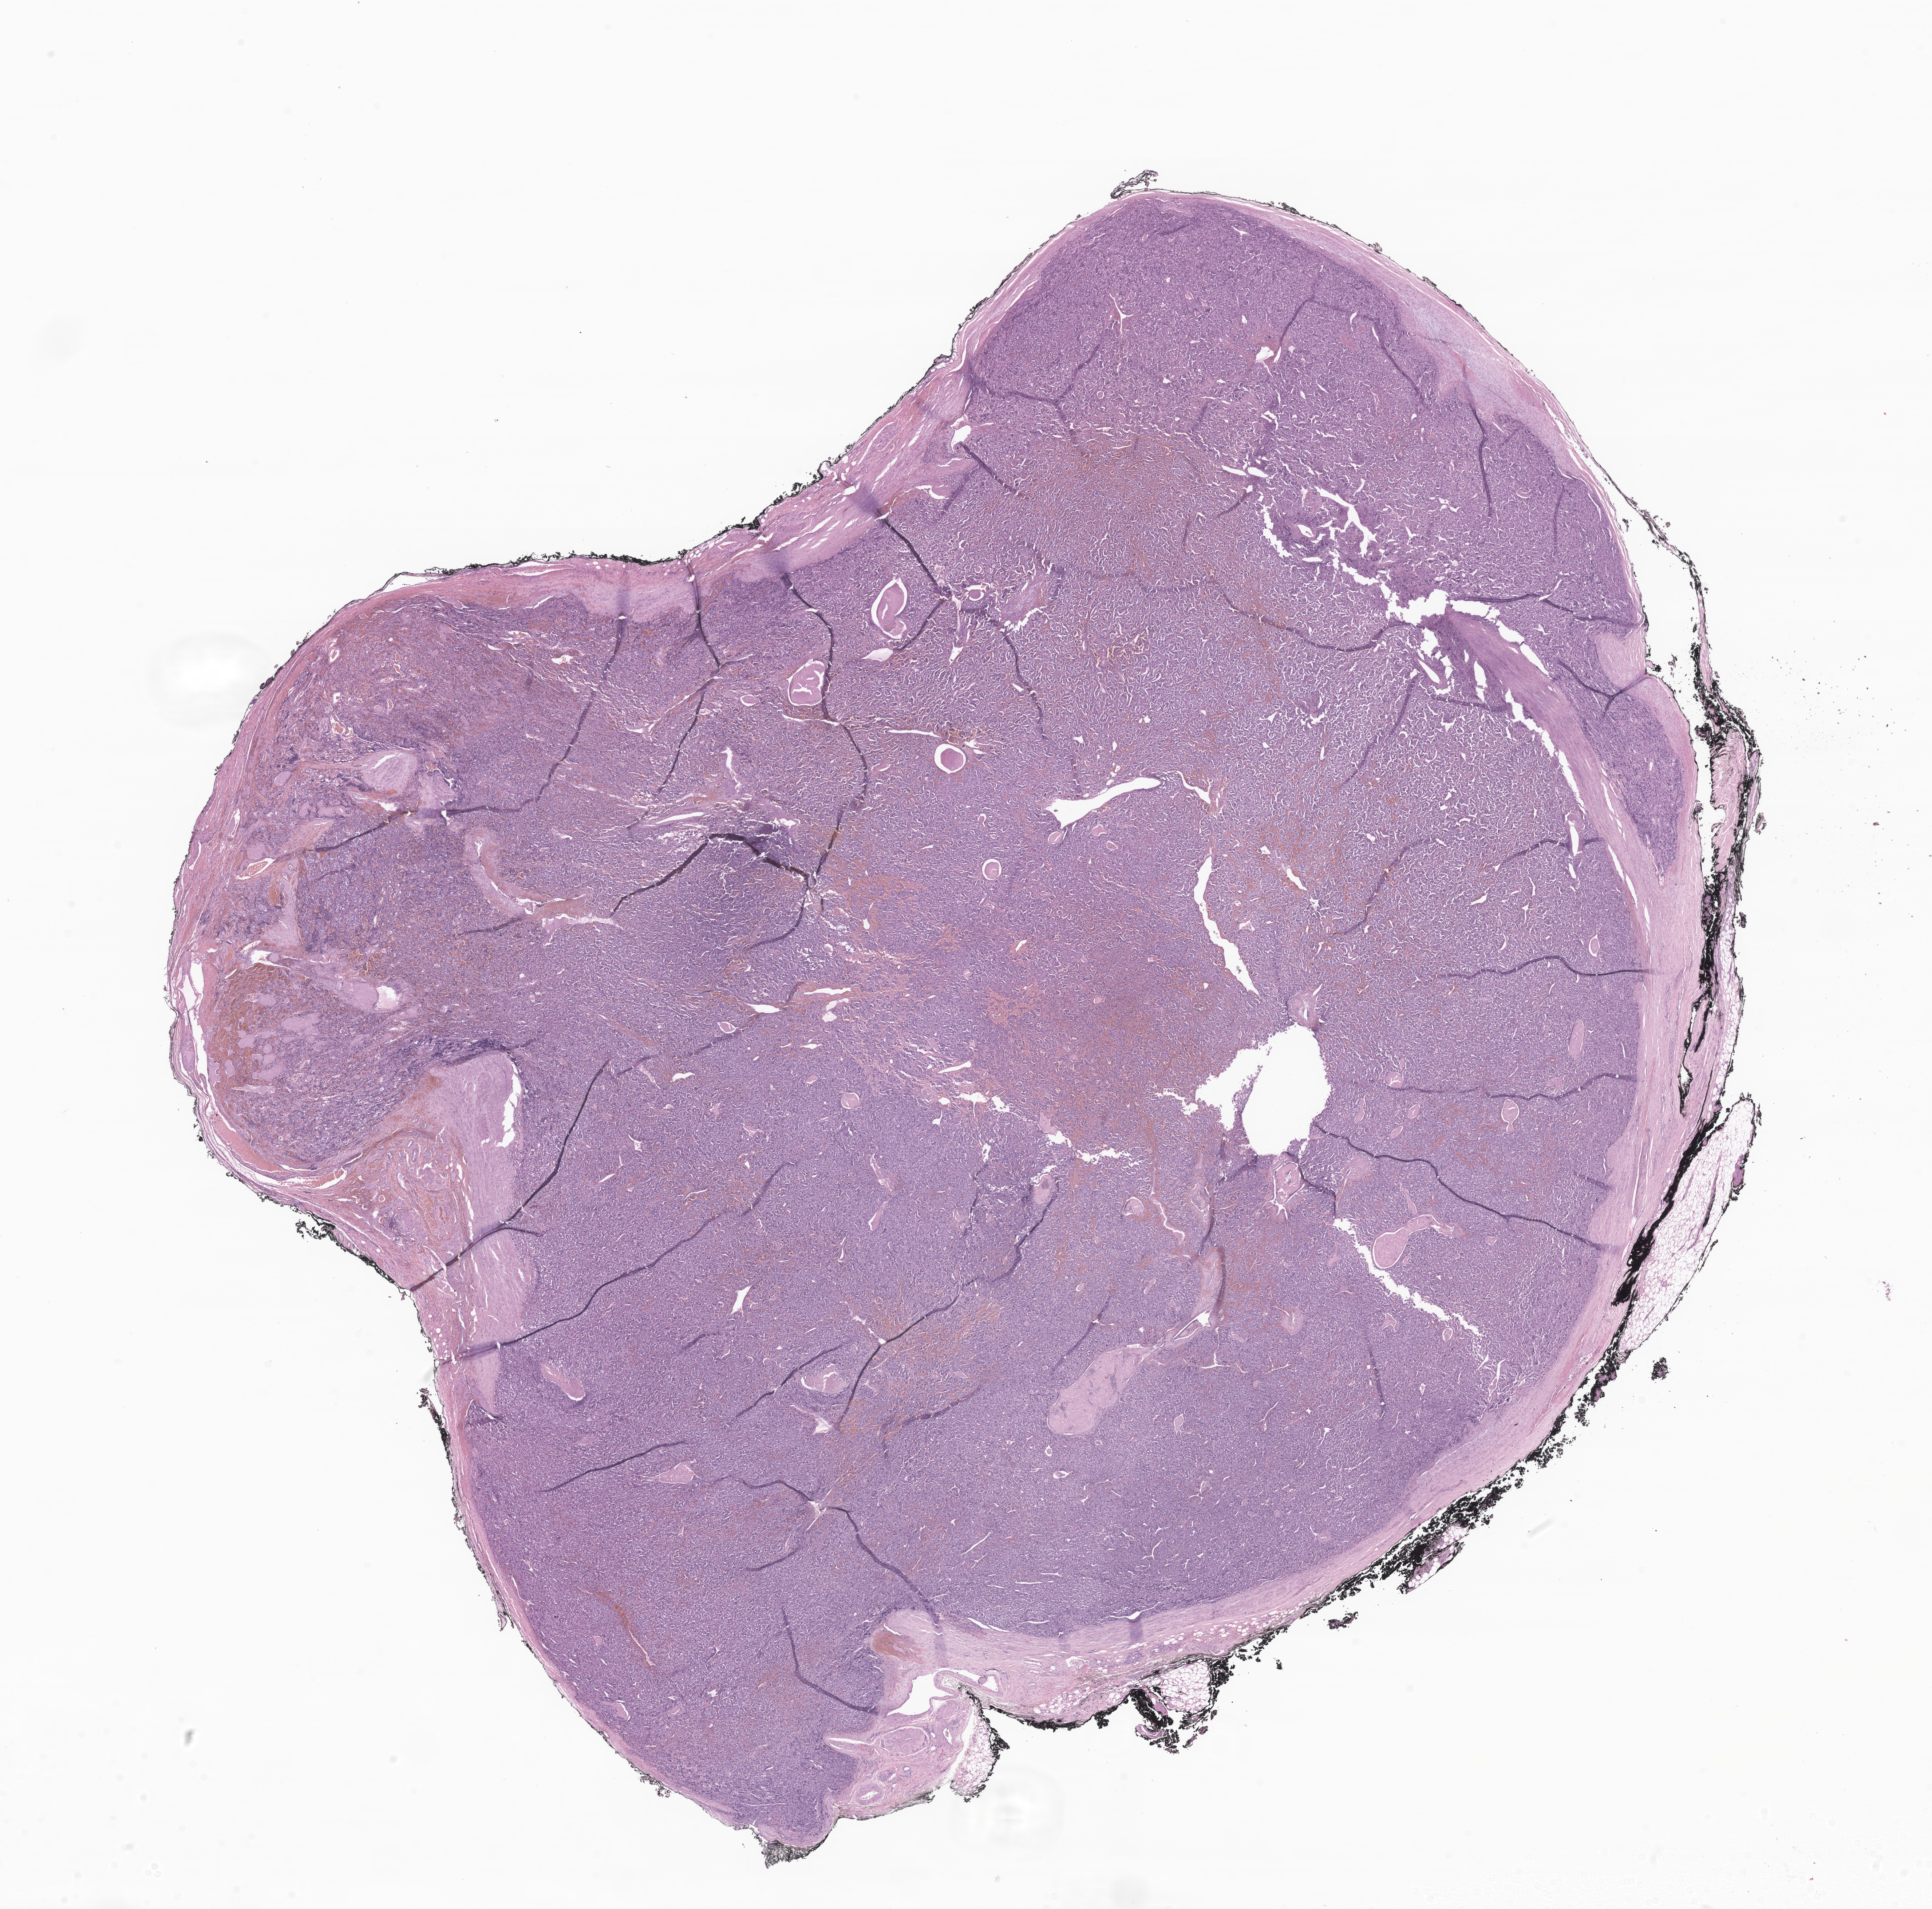
Whole-slide image, haematoxylin and eosin stain of tumor tissue from the retroperitoneum, low-resolution overview of the scanned area, about 22.4 x 22.1 mm. Formalin-fixed, paraffin-embedded (FFPE) tissue. Patient male; age 158 months.
Recorded diagnosis: Paraganglioma, NOS.